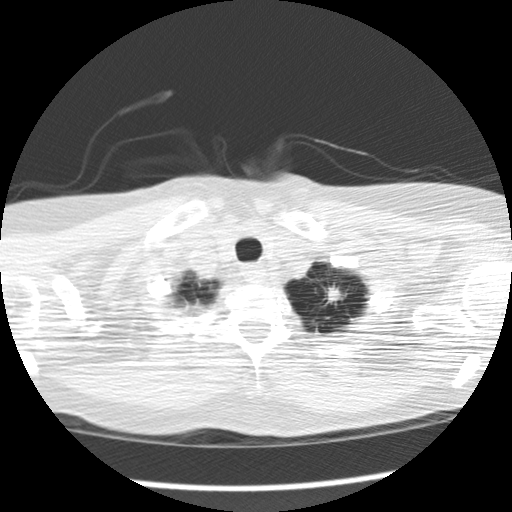
Axial slice from a low-dose chest CT screening exam; second screening round (one year after baseline); lung window (W 1500 / L -600 HU); 120 kVp; slice 150 of 159 in the series. Female, age 69 years at enrolment.
Lesion marked by an expert reader, bounding box (x1, y1, x2, y2) in pixels: (310, 275, 360, 320). The screening reader recorded 2 non-calcified nodules or masses ≥4 mm on this exam (right upper lobe, lingula); which of them this box marks is not recorded. Official screen result: positive, change unspecified: nodule(s) >= 4 mm or enlarging nodule(s), mass(es), or other non-specific abnormalities suspicious for lung cancer. Lung cancer was diagnosed 147 days after this screen: adenocarcinoma, NOS, left upper lobe, poorly differentiated (G3), stage IB (AJCC 6th edition), 80 mm at pathology.